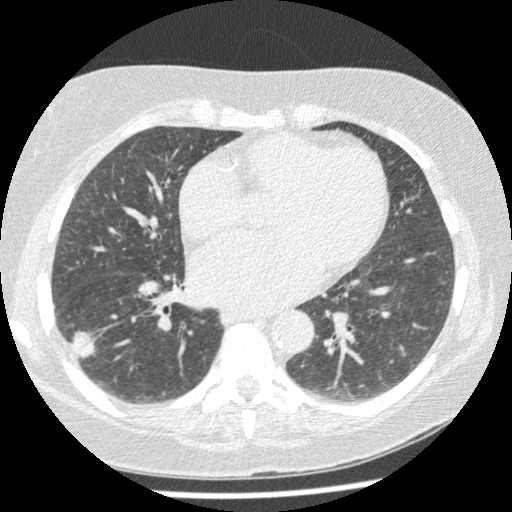
Low-dose screening chest CT, one axial slice. Position 108 of 241 along the scan axis. Reconstruction kernel STANDARD. Lung window (W 1500 / L -600 HU). 512 × 512 image matrix, field of view 305 × 305 mm.
Structures marked on this image (outlined manually by an expert reader):
- lesion 1 (tumor, lower lobe of right lung): bounding box <71,331,94,359> (left, top, right, bottom; pixels)